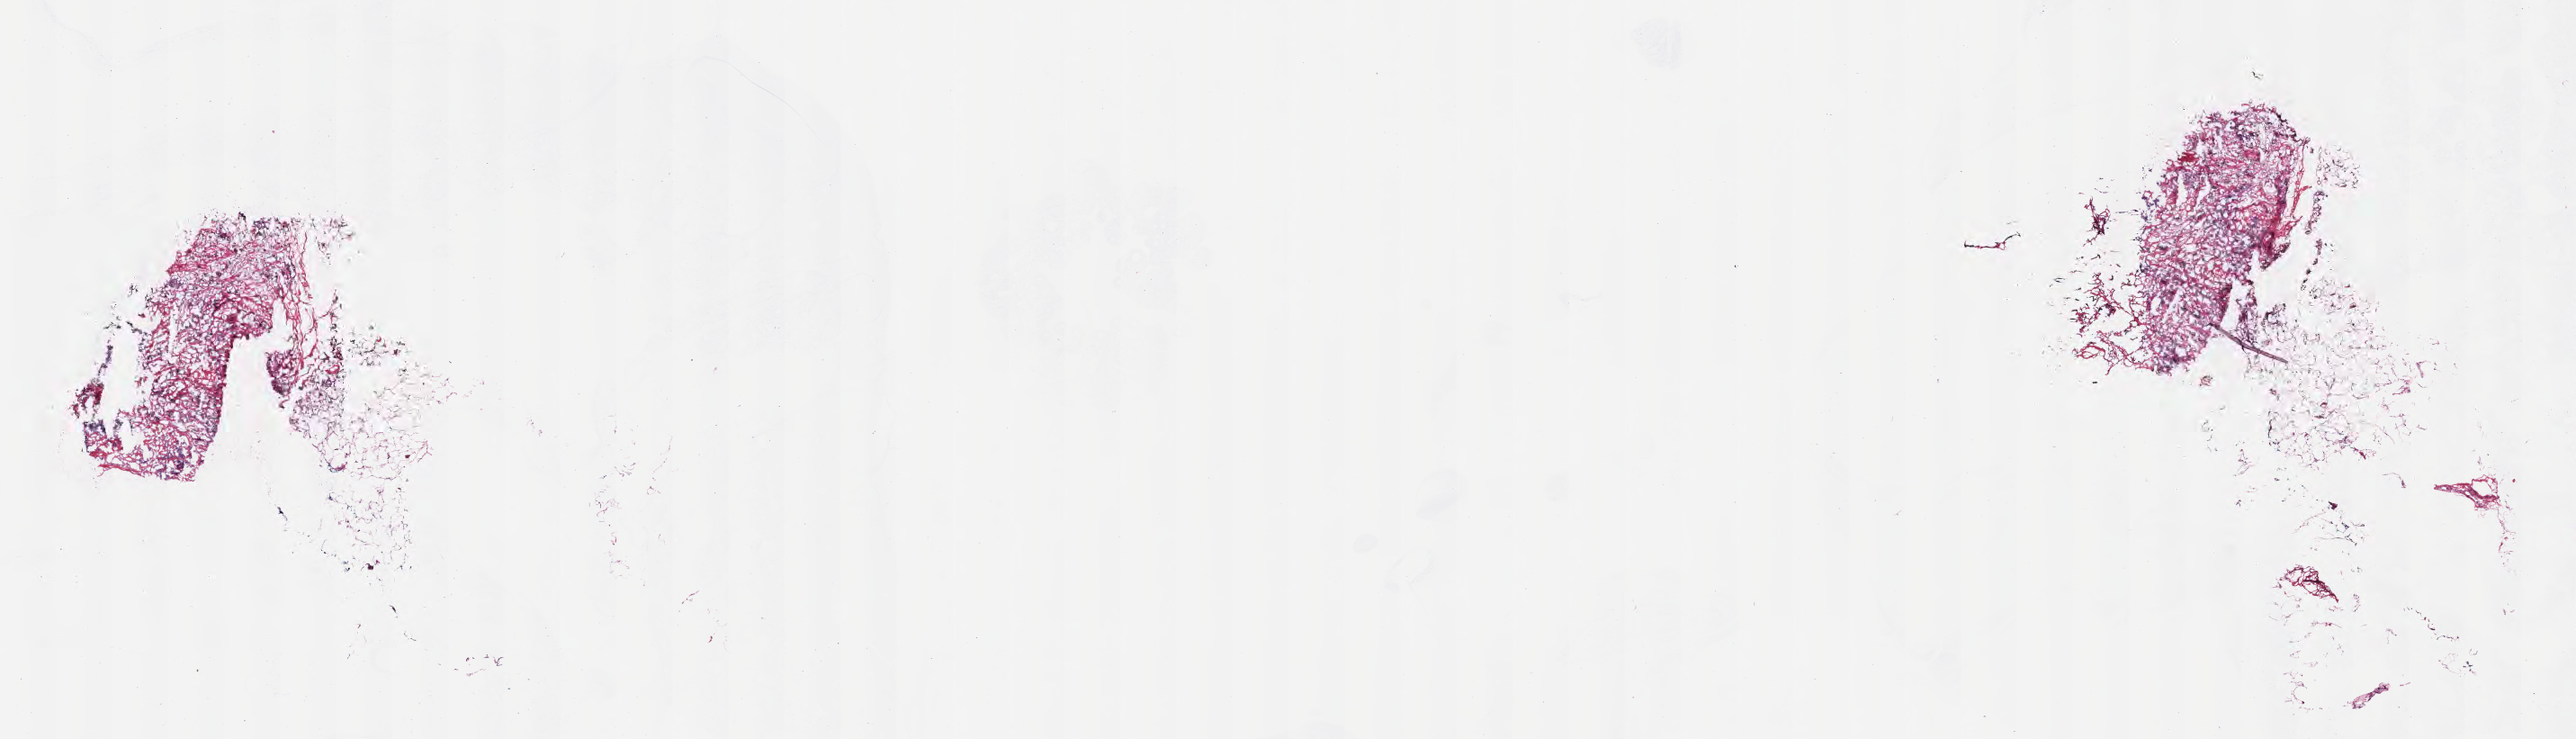
H&E whole-slide image — low-resolution overview of the scanned area, about 23.1 x 6.6 mm. Frozen section. Specimen: primary tumor. Anatomic site: breast. Female, age 52 years at initial diagnosis. Slide review estimates, as recorded: tumor cells 80%, tumor nuclei 80%, stromal cells 20%, necrosis 0%, normal cells 0%. Inflammatory infiltration, as recorded: lymphocyte infiltration 3%, monocyte infiltration 2%, neutrophil infiltration 6%.
Section: bottom of the tissue portion. Histologic diagnosis: Infiltrating duct carcinoma, NOS. AJCC pathologic stage: Stage IIA.